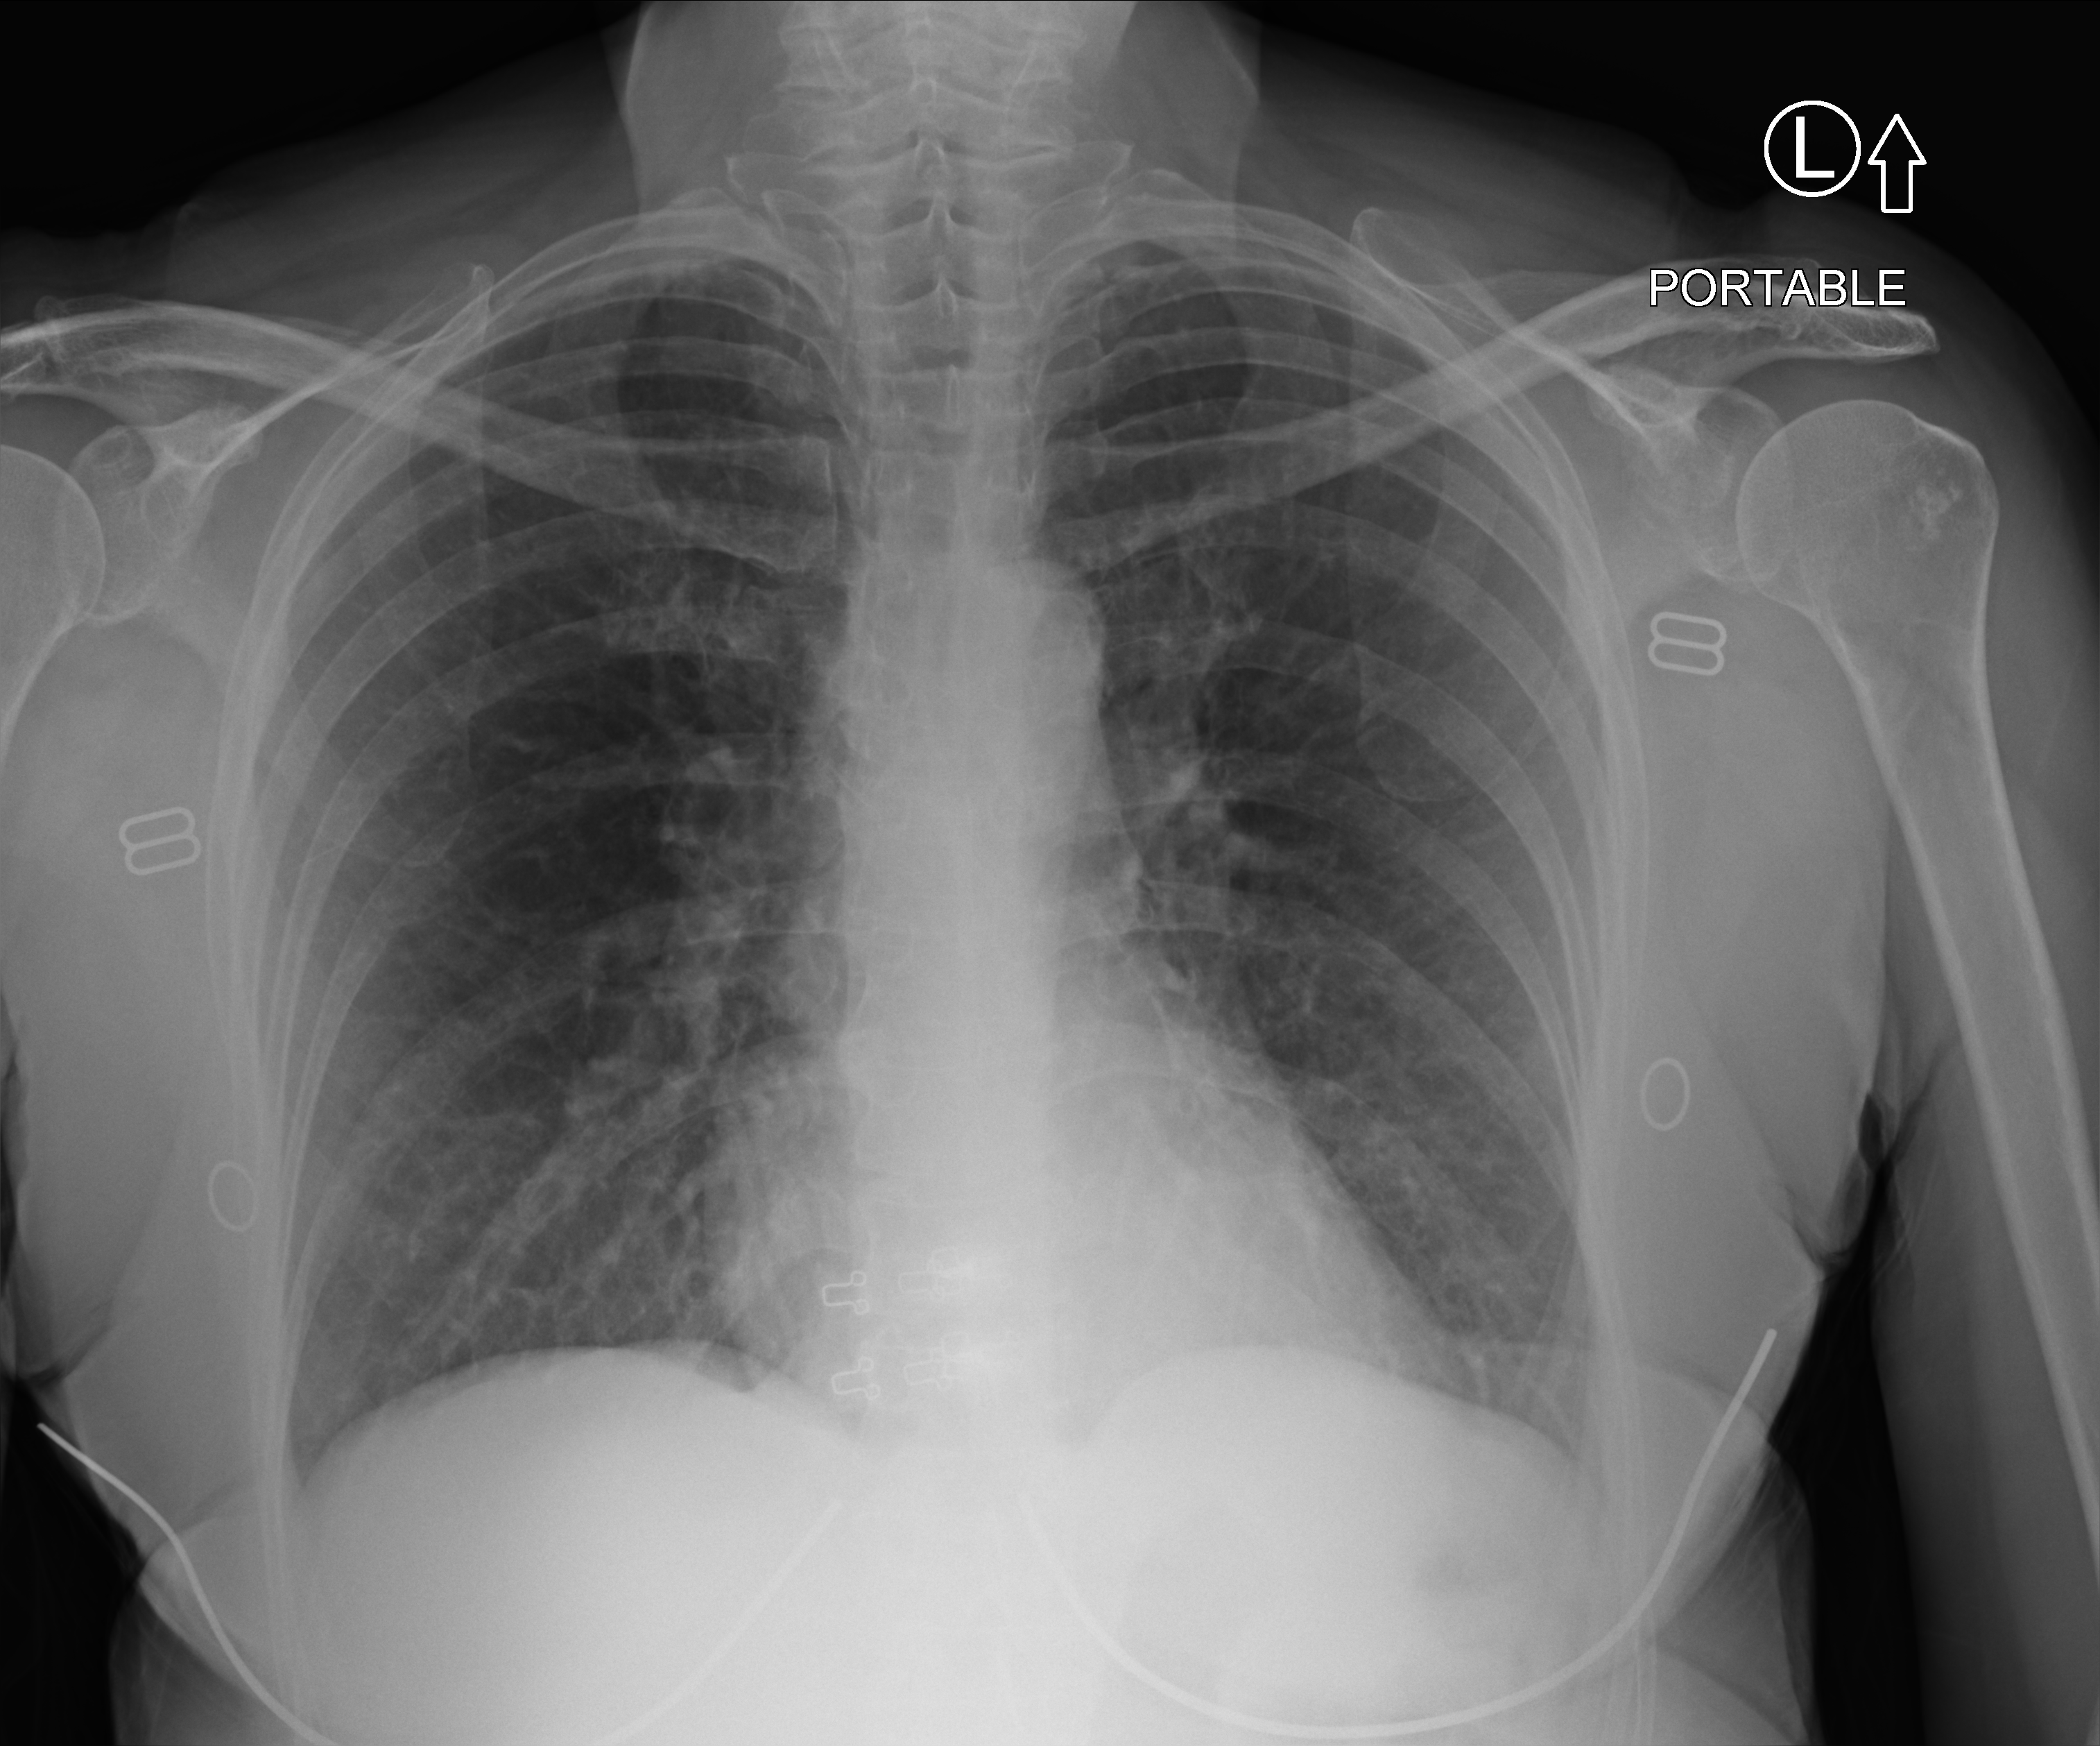
Bedside chest radiograph (computed radiography); anteroposterior (AP) projection. Patient hospitalised with COVID-19; female, aged 60–74 years.
Hospital-stay facts (about this admission, not read from this image; timing relative to this image not recorded):
- length of hospital stay: 1 day